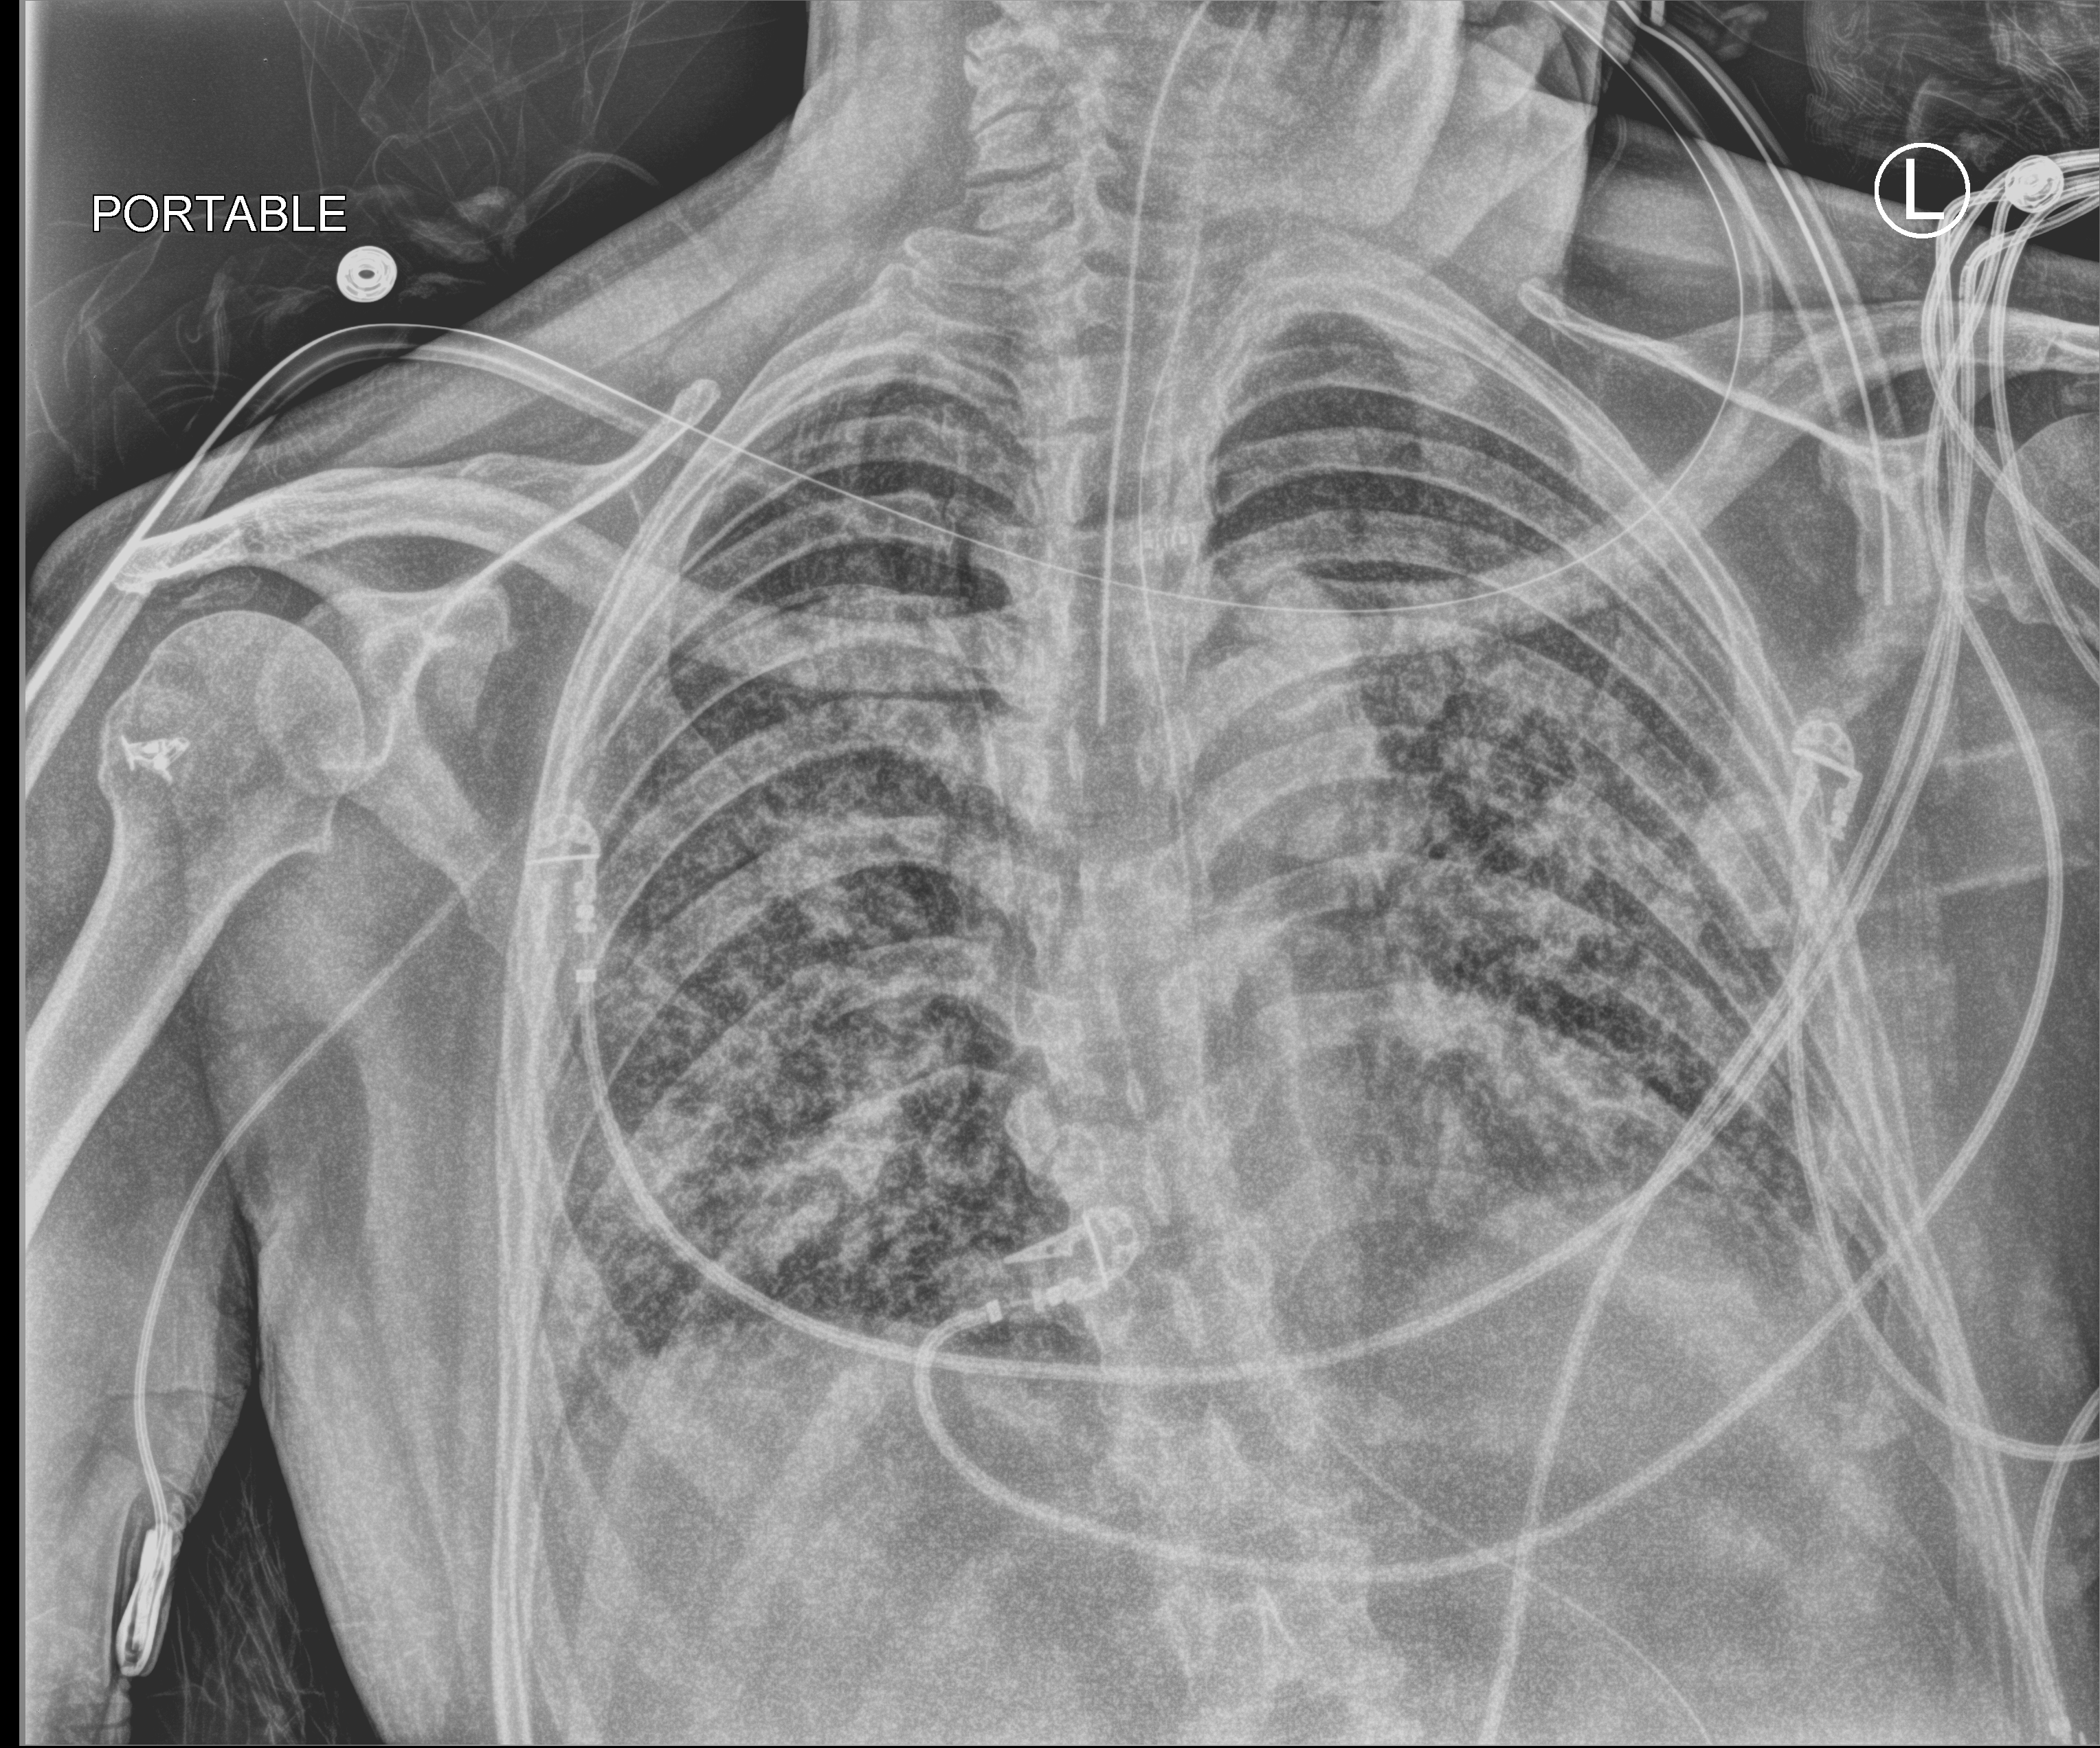
Bedside chest radiograph (computed radiography). Patient hospitalised with COVID-19; male, aged 60–74 years.
Admission-level facts for this patient (not findings on this image; timing relative to this image not recorded): COPD (admission record): no; mechanically ventilated during this hospital stay: yes.